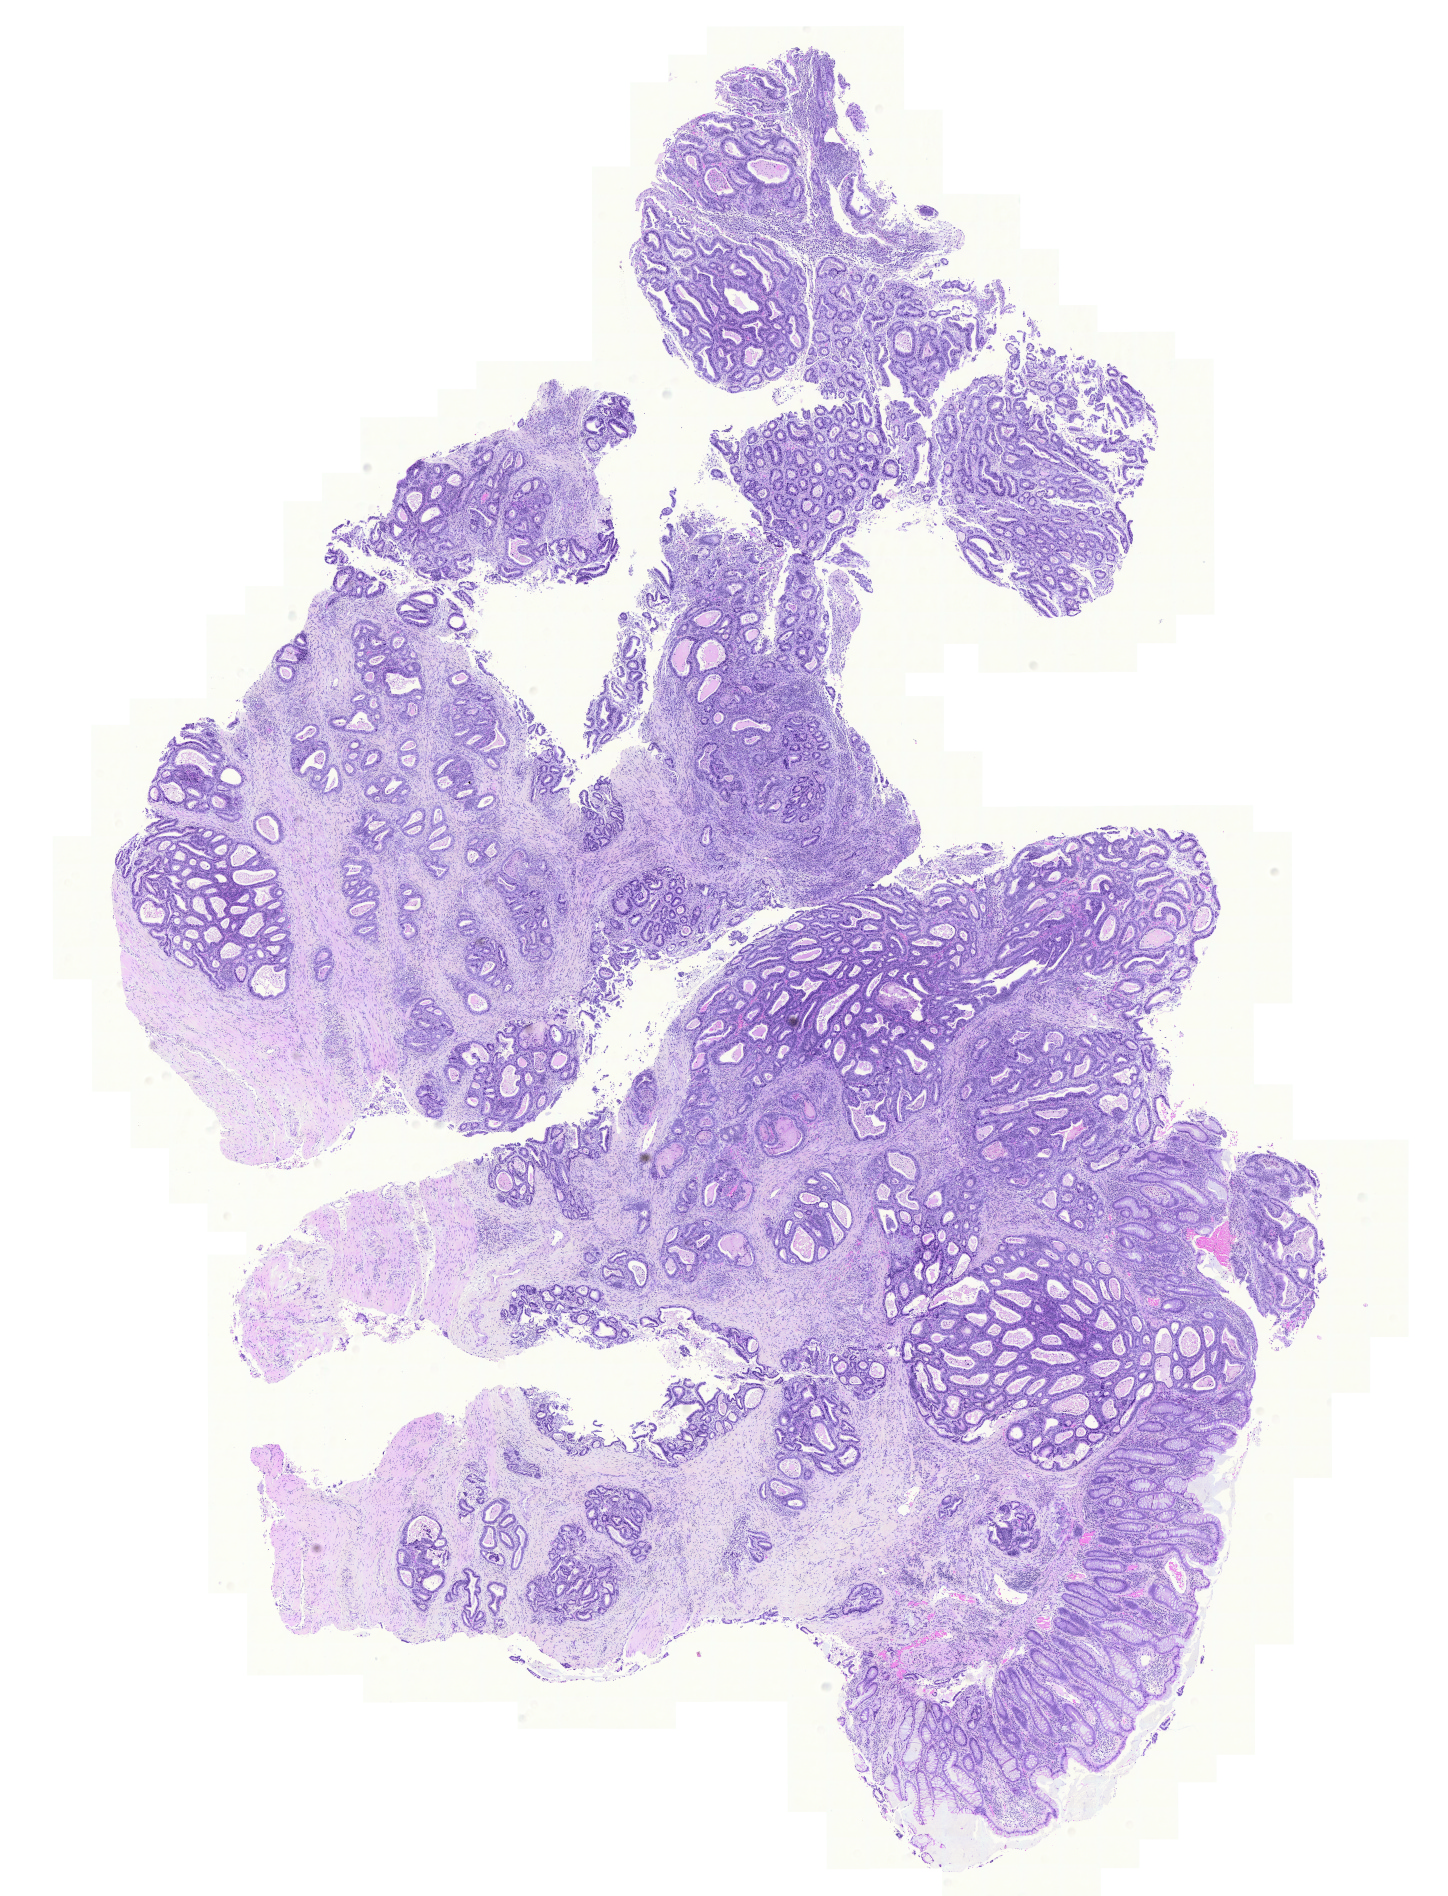
Whole-slide histology image, Hematoxylin and eosin (H&E) stained — whole scanned area (about 10.8 x 14.1 mm, slide scanned at 20x) shown as a low-resolution overview. Formalin-fixed paraffin-embedded (FFPE) diagnostic section. Sample: primary tumour, colon. Male, age 76 years at initial diagnosis.
TNM: T3 N0 M0. AJCC pathologic stage: IIA (6th edition). Histologic diagnosis: Adenocarcinoma, NOS (sigmoid colon).